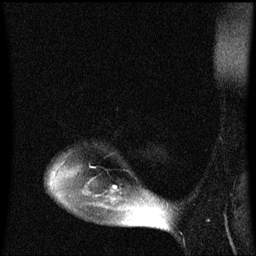
Breast MRI (dynamic contrast-enhanced), one sagittal slice; position 49 of 60 along the scan axis; dynamic contrast-enhanced series, image 2 of 3 at this slice position (ordered by acquisition); 1.5 T; TE 4.2 ms, TR 8.4 ms; 256 × 256 image matrix, field of view 200 × 200 mm. Female patient, age 49 years. Case-level facts recorded for this patient, not image findings: setting: breast cancer imaged before/during neoadjuvant chemotherapy; receptor status: HR-positive, HER2-negative.
Annotated regions visible in this slice (semi-automatically segmented with operator editing):
- analysis volume of interest (the breast-tissue region the enhancement analysis was run in; not a lesion): box from (x=49, y=150) to (x=174, y=221) px
- tumour enhancement mask (voxels above the 70 % enhancement threshold inside the analysis volume of interest): (x=114, y=186)–(x=117, y=189)